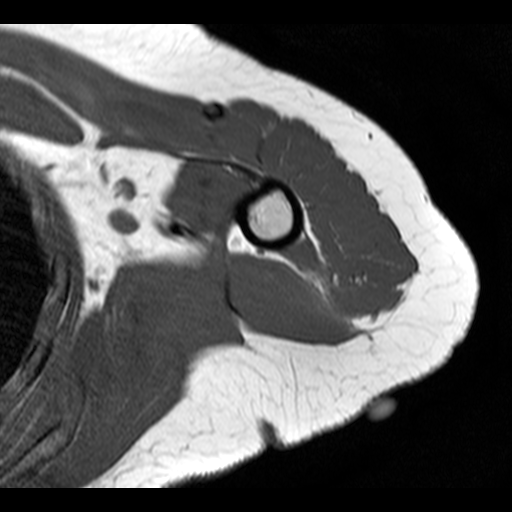
MRI of an extremity soft-tissue mass, one axial slice. 4 mm slice thickness. 512 × 512 image matrix, field of view 150 × 150 mm. Female patient. Case-level facts recorded for this patient, not image findings: histological type: malignant fibrous histiocytoma; grade: low; site of the primary tumour: left arm.
Outlined on this slice (expert manual segmentation):
- gross tumour volume (mass): bounding box <308,271,343,325> (left, top, right, bottom; pixels)